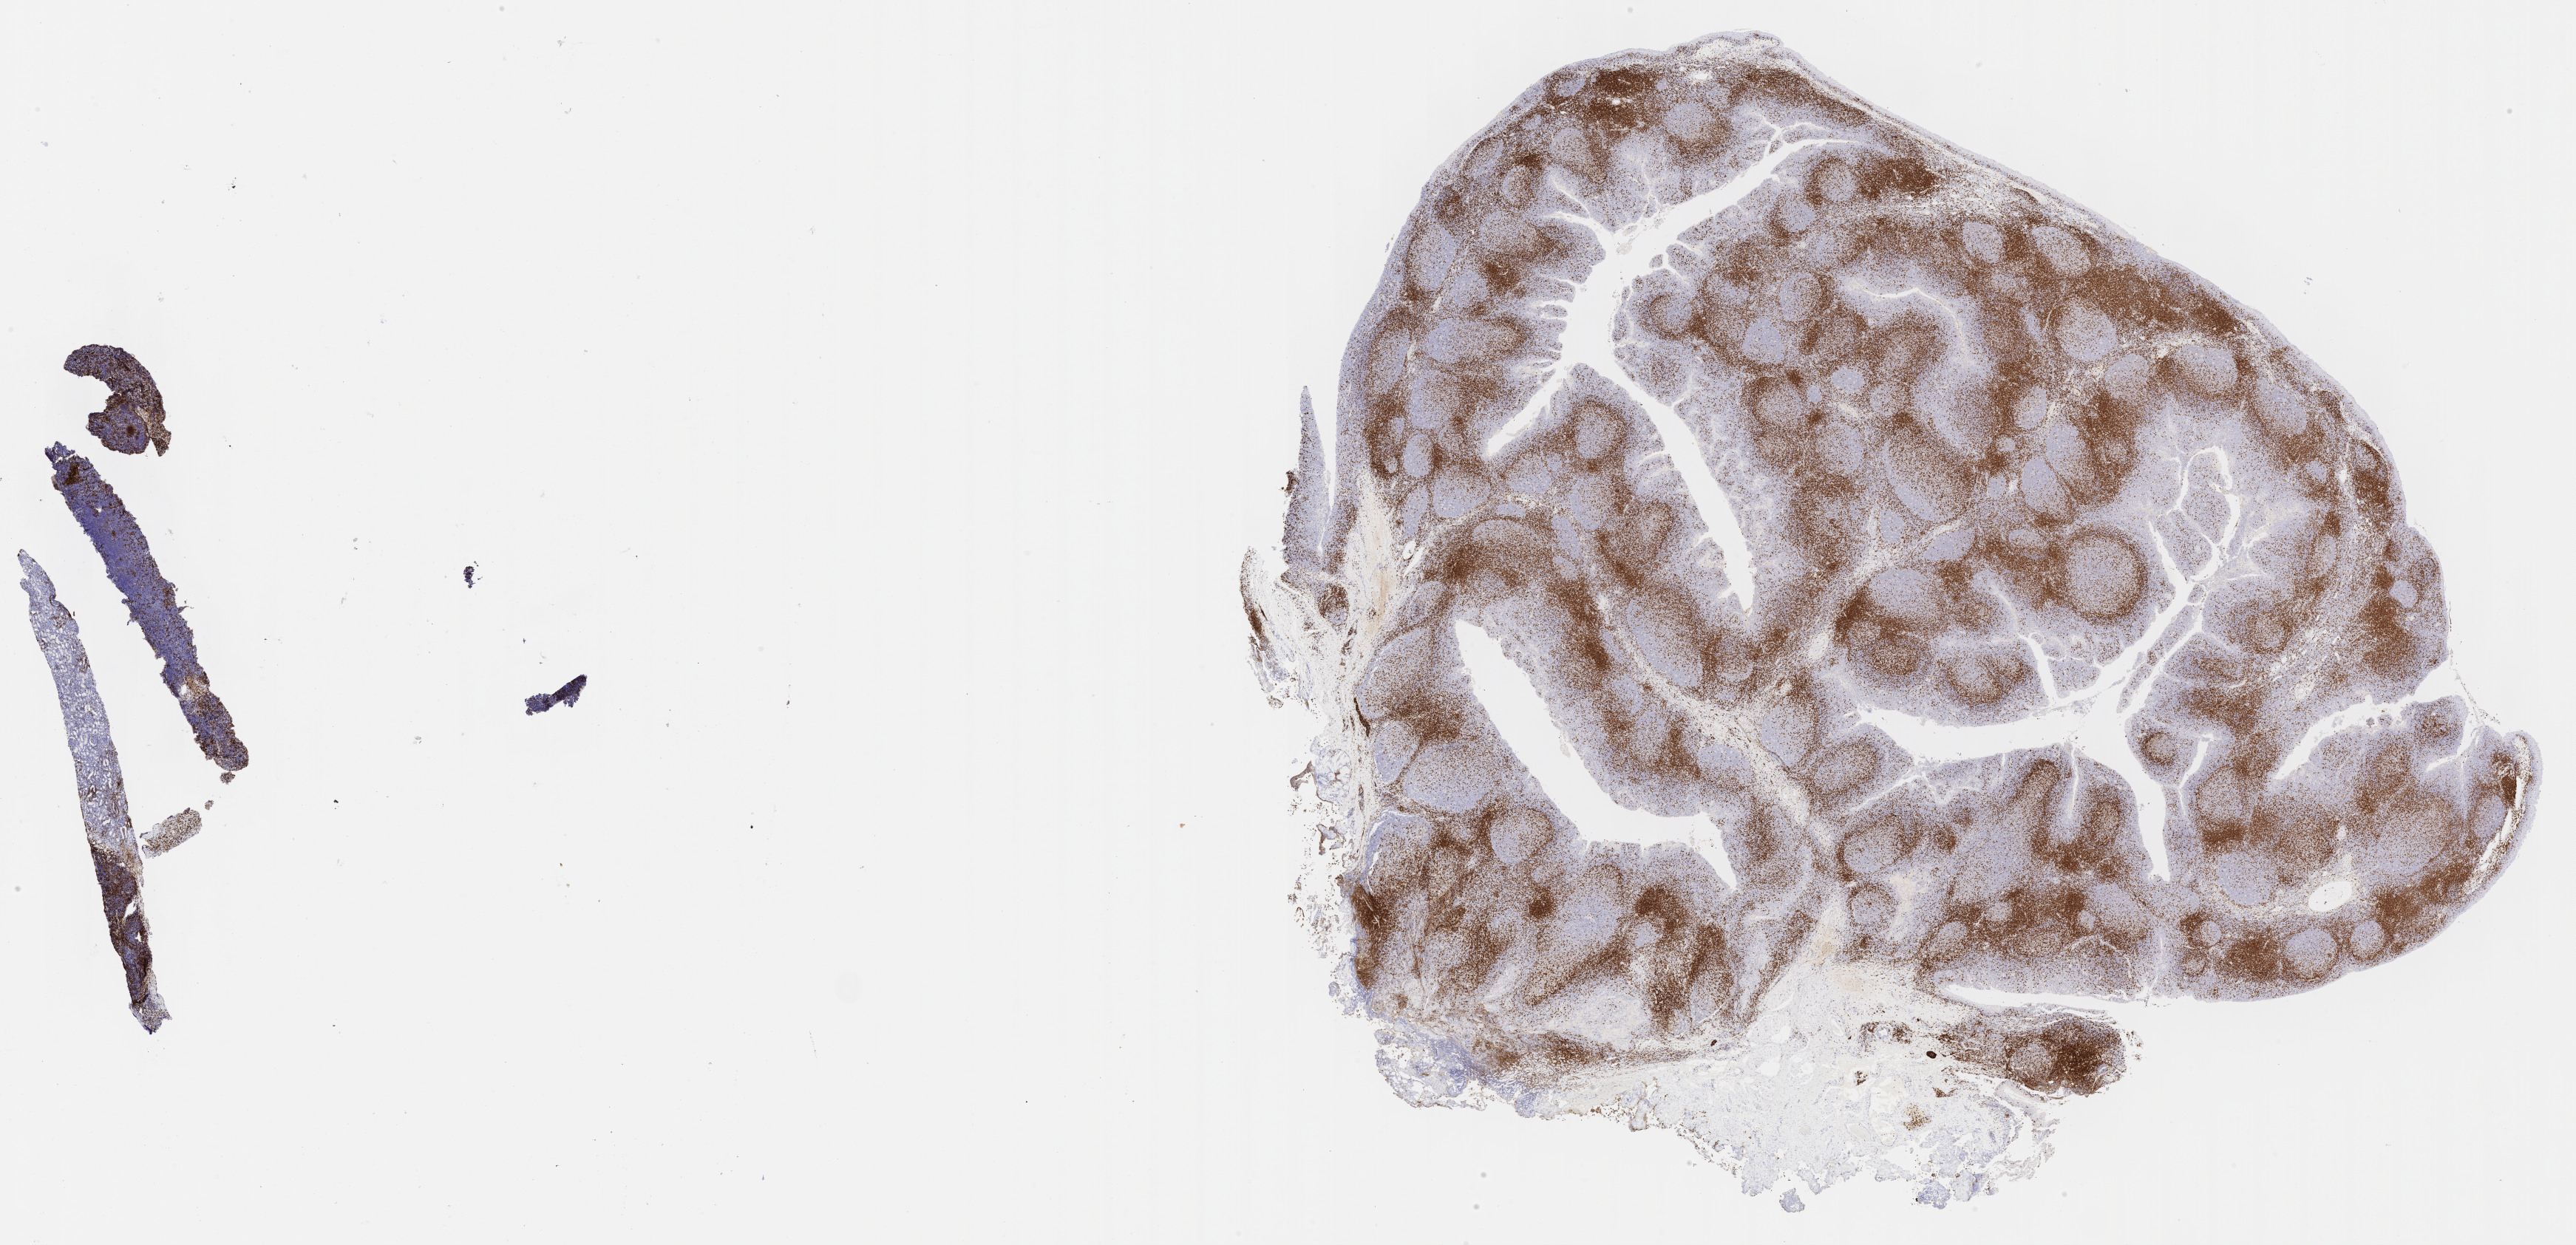
IHC for CD3, whole-slide image, whole scanned area (about 28.2 x 13.6 mm) shown as a low-resolution overview; specimen: tumor tissue; anatomic site: liver. Patient: male, age at initial diagnosis 8 years.
Histologic diagnosis: Burkitt lymphoma, NOS.